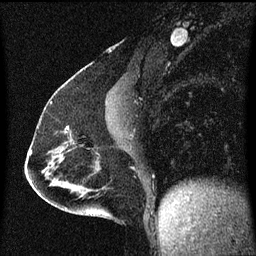
Breast MRI (dynamic contrast-enhanced), one sagittal slice. Dynamic contrast-enhanced series, image 2 of 3 at this slice position (ordered by acquisition). 1.5 T. TE 4.2 ms, TR 8 ms. 2 mm slice thickness. 256 × 256 image matrix, field of view 200 × 200 mm. Patient: female, 51 years.
Outlined on this slice (semi-automatically segmented with operator editing):
- analysis volume of interest (the breast-tissue region the enhancement analysis was run in; not a lesion): bounding box [x1, y1, x2, y2] px = [62, 126, 87, 149]
- tumour enhancement mask (voxels above the 70 % enhancement threshold inside the analysis volume of interest): [66, 126, 71, 133]